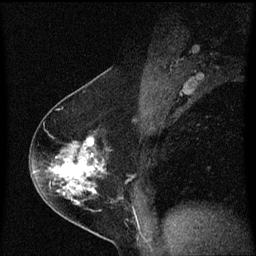
Breast MRI (dynamic contrast-enhanced), one sagittal slice; position 37 of 60 along the scan axis; dynamic contrast-enhanced series, image 2 of 3 at this slice position (ordered by acquisition); 1.5 T; TE 4.2 ms, TR 8.4 ms; 256 × 256 image matrix, field of view 200 × 200 mm. Patient: female, 54 years. Case-level facts recorded for this patient, not image findings: setting: breast cancer imaged before/during neoadjuvant chemotherapy; receptor status: HER2-positive.
Annotated regions visible in this slice (semi-automatically segmented with operator editing):
- analysis volume of interest (the breast-tissue region the enhancement analysis was run in; not a lesion): bounding box <32,138,113,213> (left, top, right, bottom; pixels)
- tumour enhancement mask (voxels above the 70 % enhancement threshold inside the analysis volume of interest): <54,138,99,193>